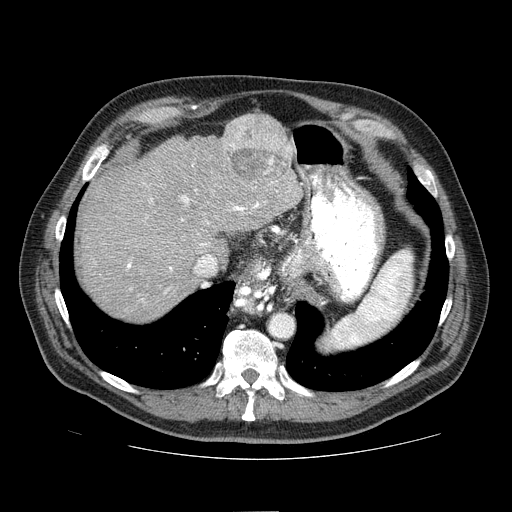
Contrast-enhanced abdominal CT (liver protocol), one axial slice. Slice 58 of 81 in the series (ordered by position). Reconstruction kernel STANDARD. One of 2 acquisitions stored at this slice position. Soft-tissue window (W 400 / L 40 HU). 512 × 512 image matrix, field of view 400 × 400 mm. Case-level facts recorded for this patient, not image findings: diagnosis: hepatocellular carcinoma (patient treated with transarterial chemoembolisation; whether this scan precedes or follows treatment is not stated here); TNM stage (as recorded): Stage-IIIA; Child-Pugh class: A; tumour nodularity: multinodular.
Annotated regions visible in this slice (semi-automatic segmentation, software-assisted and operator-edited):
- abdominal aorta: bounding box (x1, y1, x2, y2) in pixels: (271, 315, 293, 337)
- liver parenchyma outside the tumour (the mass and vessels are separate outlines, so this box may not span the whole liver): (78, 114, 302, 320)
- mass: (220, 113, 292, 186)
- liver vessels: (127, 185, 291, 301)